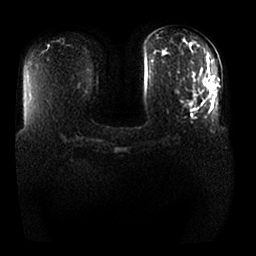
Breast MRI, one axial slice; slice 9 of 25 in the series (ordered by position); diffusion-weighted series; image 2 of 4 stored at this slice position (different b-values; order by instance number); 1.5 T; 256 × 256 image matrix, field of view 370 × 370 mm. Female patient.
Annotated regions visible in this slice (expert manual segmentation):
- tumour on diffusion-weighted imaging: bounding box <184,102,193,109> (left, top, right, bottom; pixels)